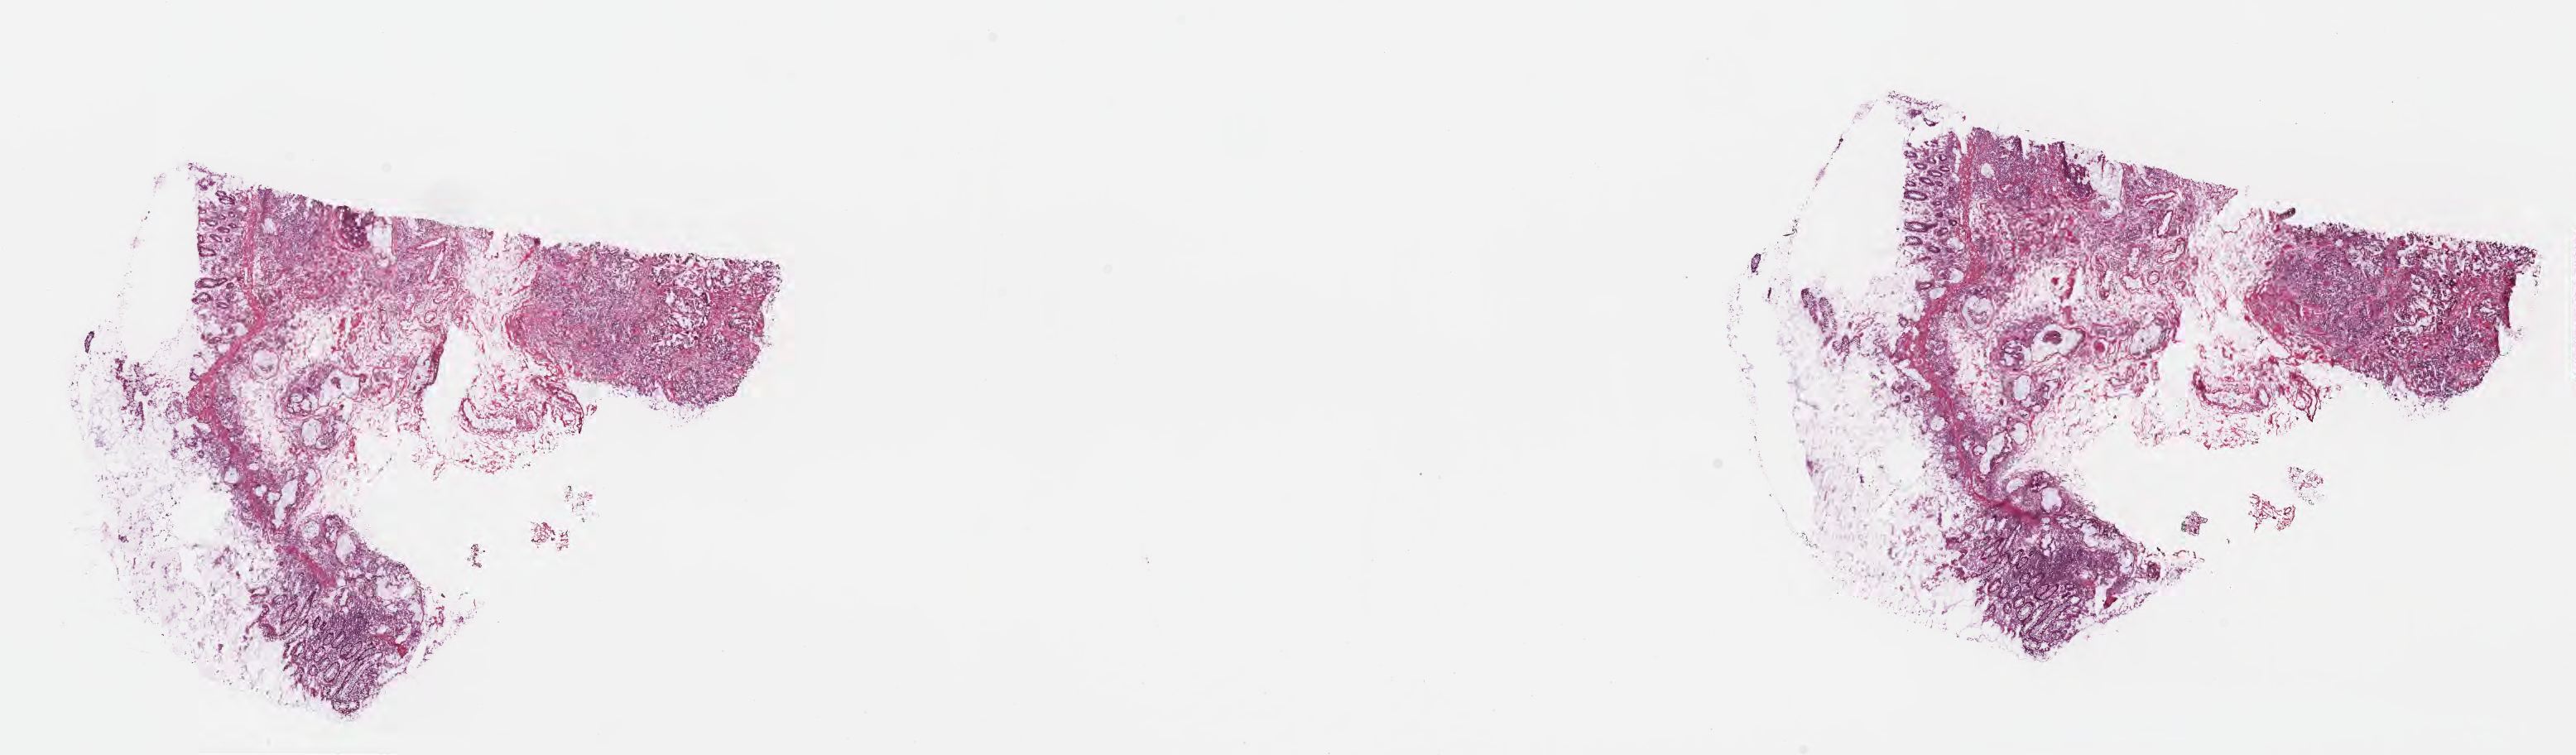
Digitized haematoxylin and eosin-stained section — whole scanned area (about 25.1 x 7.4 mm) shown as a low-resolution overview, cryosection, primary tumor, anatomic site: hepatic flexure of colon. Male, age 69 years at initial diagnosis. Tumor grade: G2 (moderately differentiated). Slide review estimates, as recorded: tumor cells 75%, tumor nuclei 75%, stromal cells 18%, necrosis 1%, normal cells 6%. Infiltration values recorded for this section: lymphocyte infiltration 4%, monocyte infiltration 3%, neutrophil infiltration 6%.
• AJCC pathologic stage: Stage IIIC
• histologic diagnosis: Mucinous adenocarcinoma
• section: bottom of the tissue portion